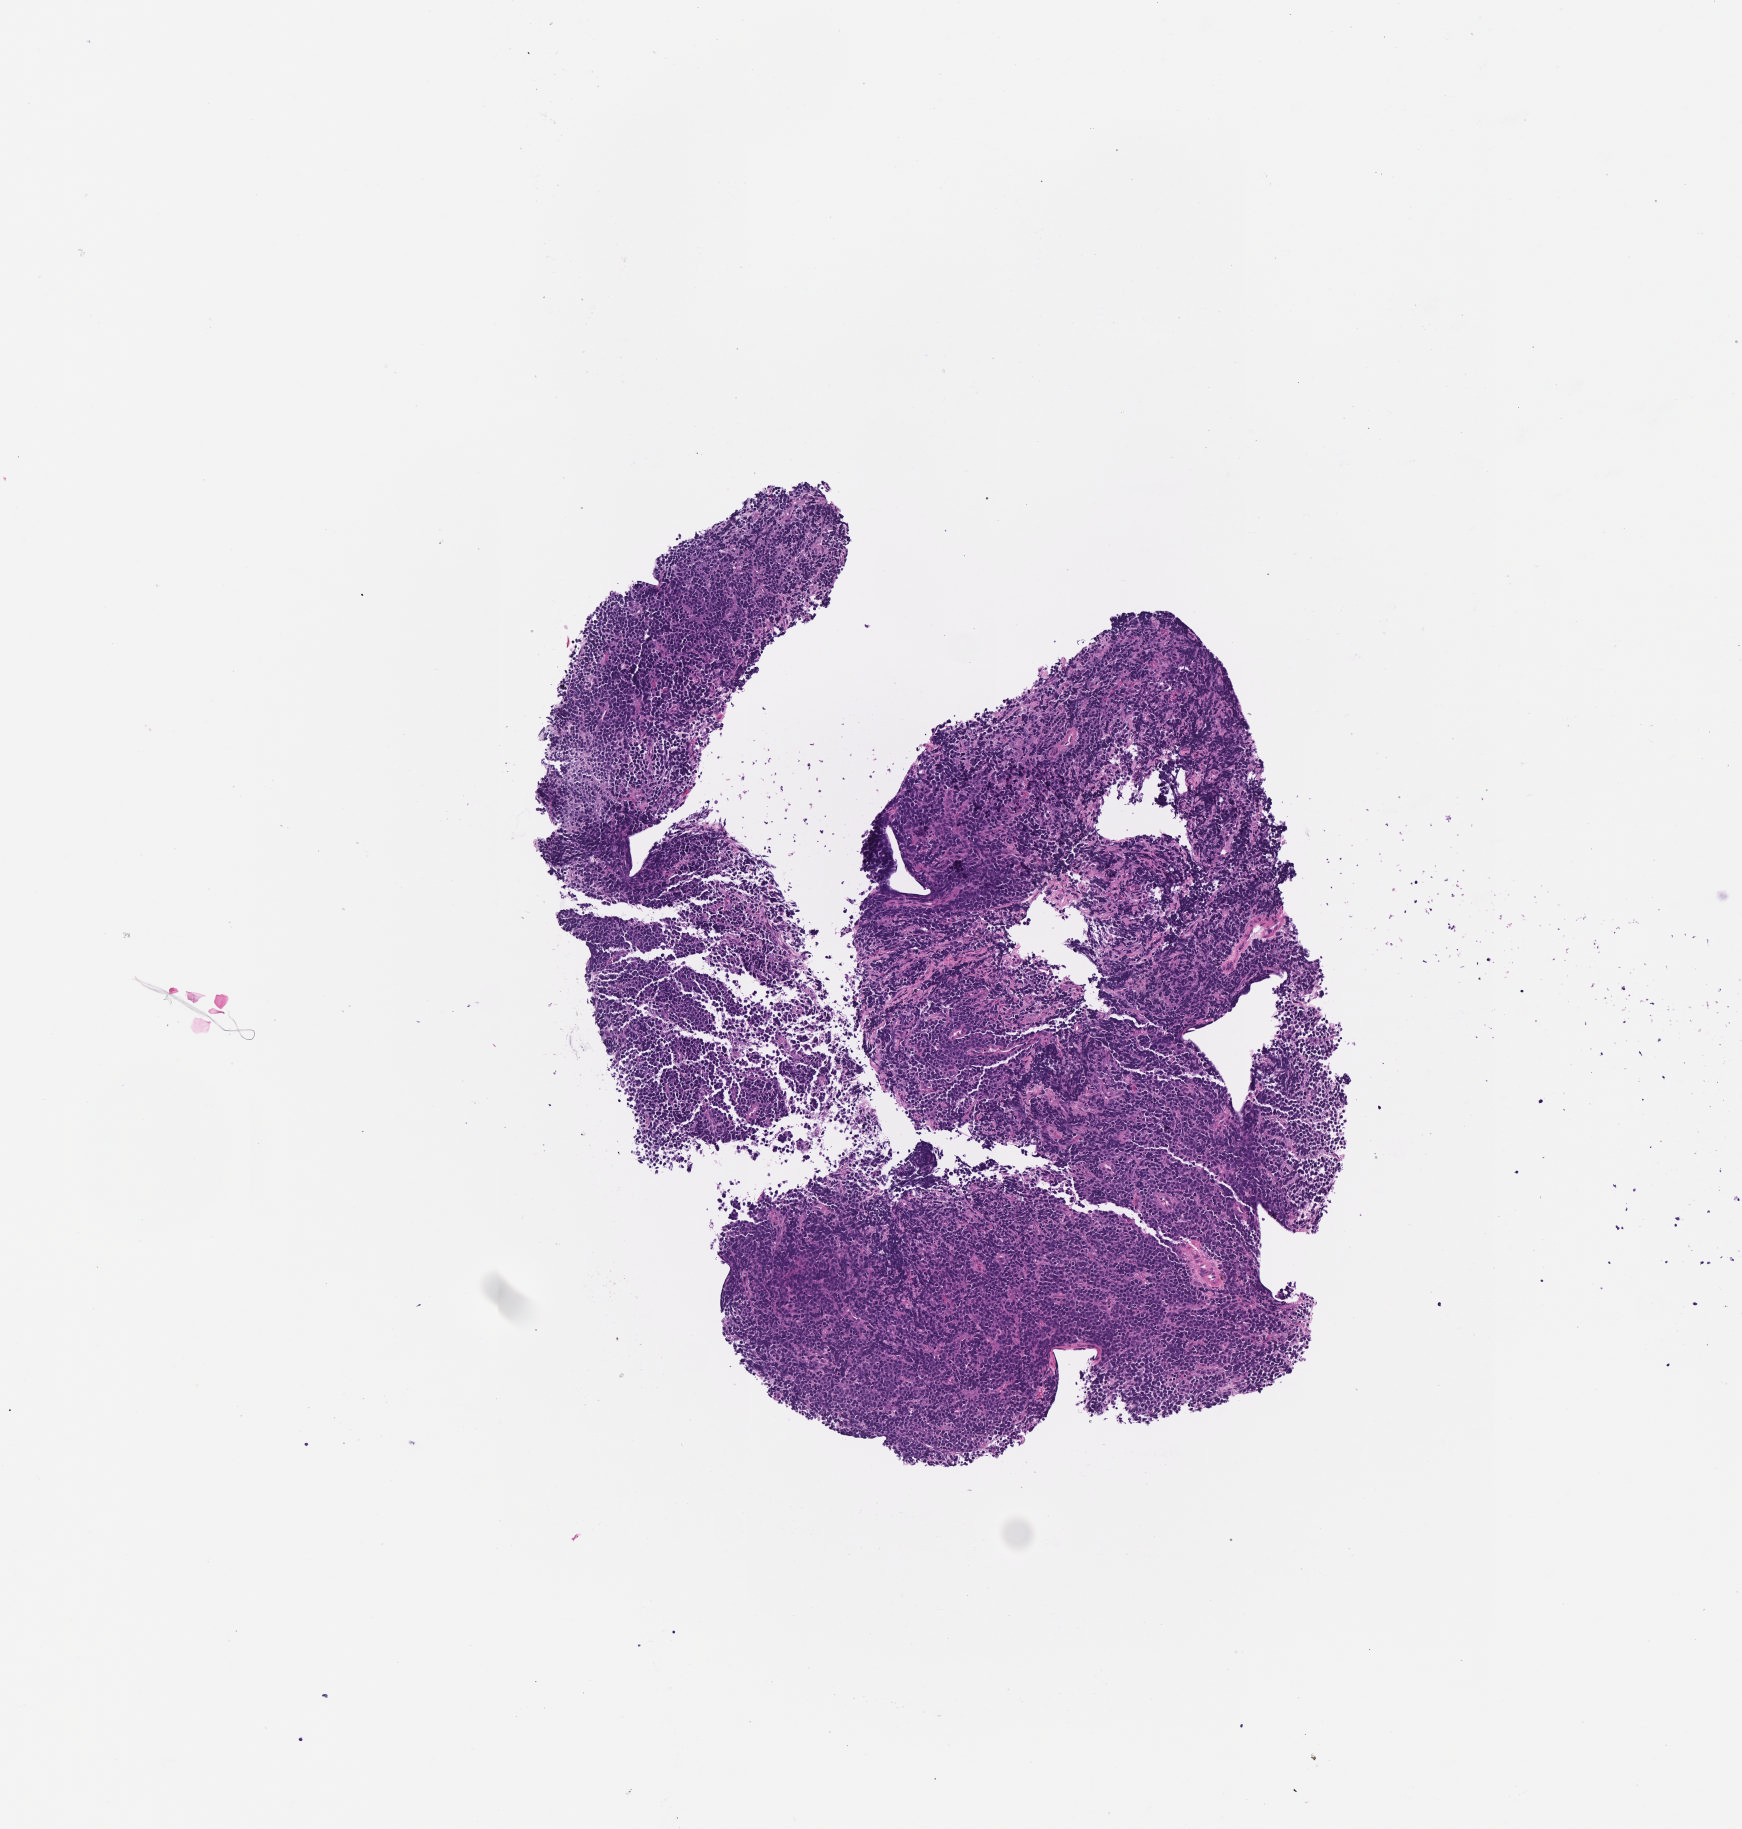
Hematoxylin and eosin (H&E) whole-slide image, whole scanned area (about 3.5 x 3.7 mm) shown as a low-resolution overview. Tumor tissue. Patient: female, age at initial diagnosis 8 years.
Diagnosis: Burkitt lymphoma, NOS.